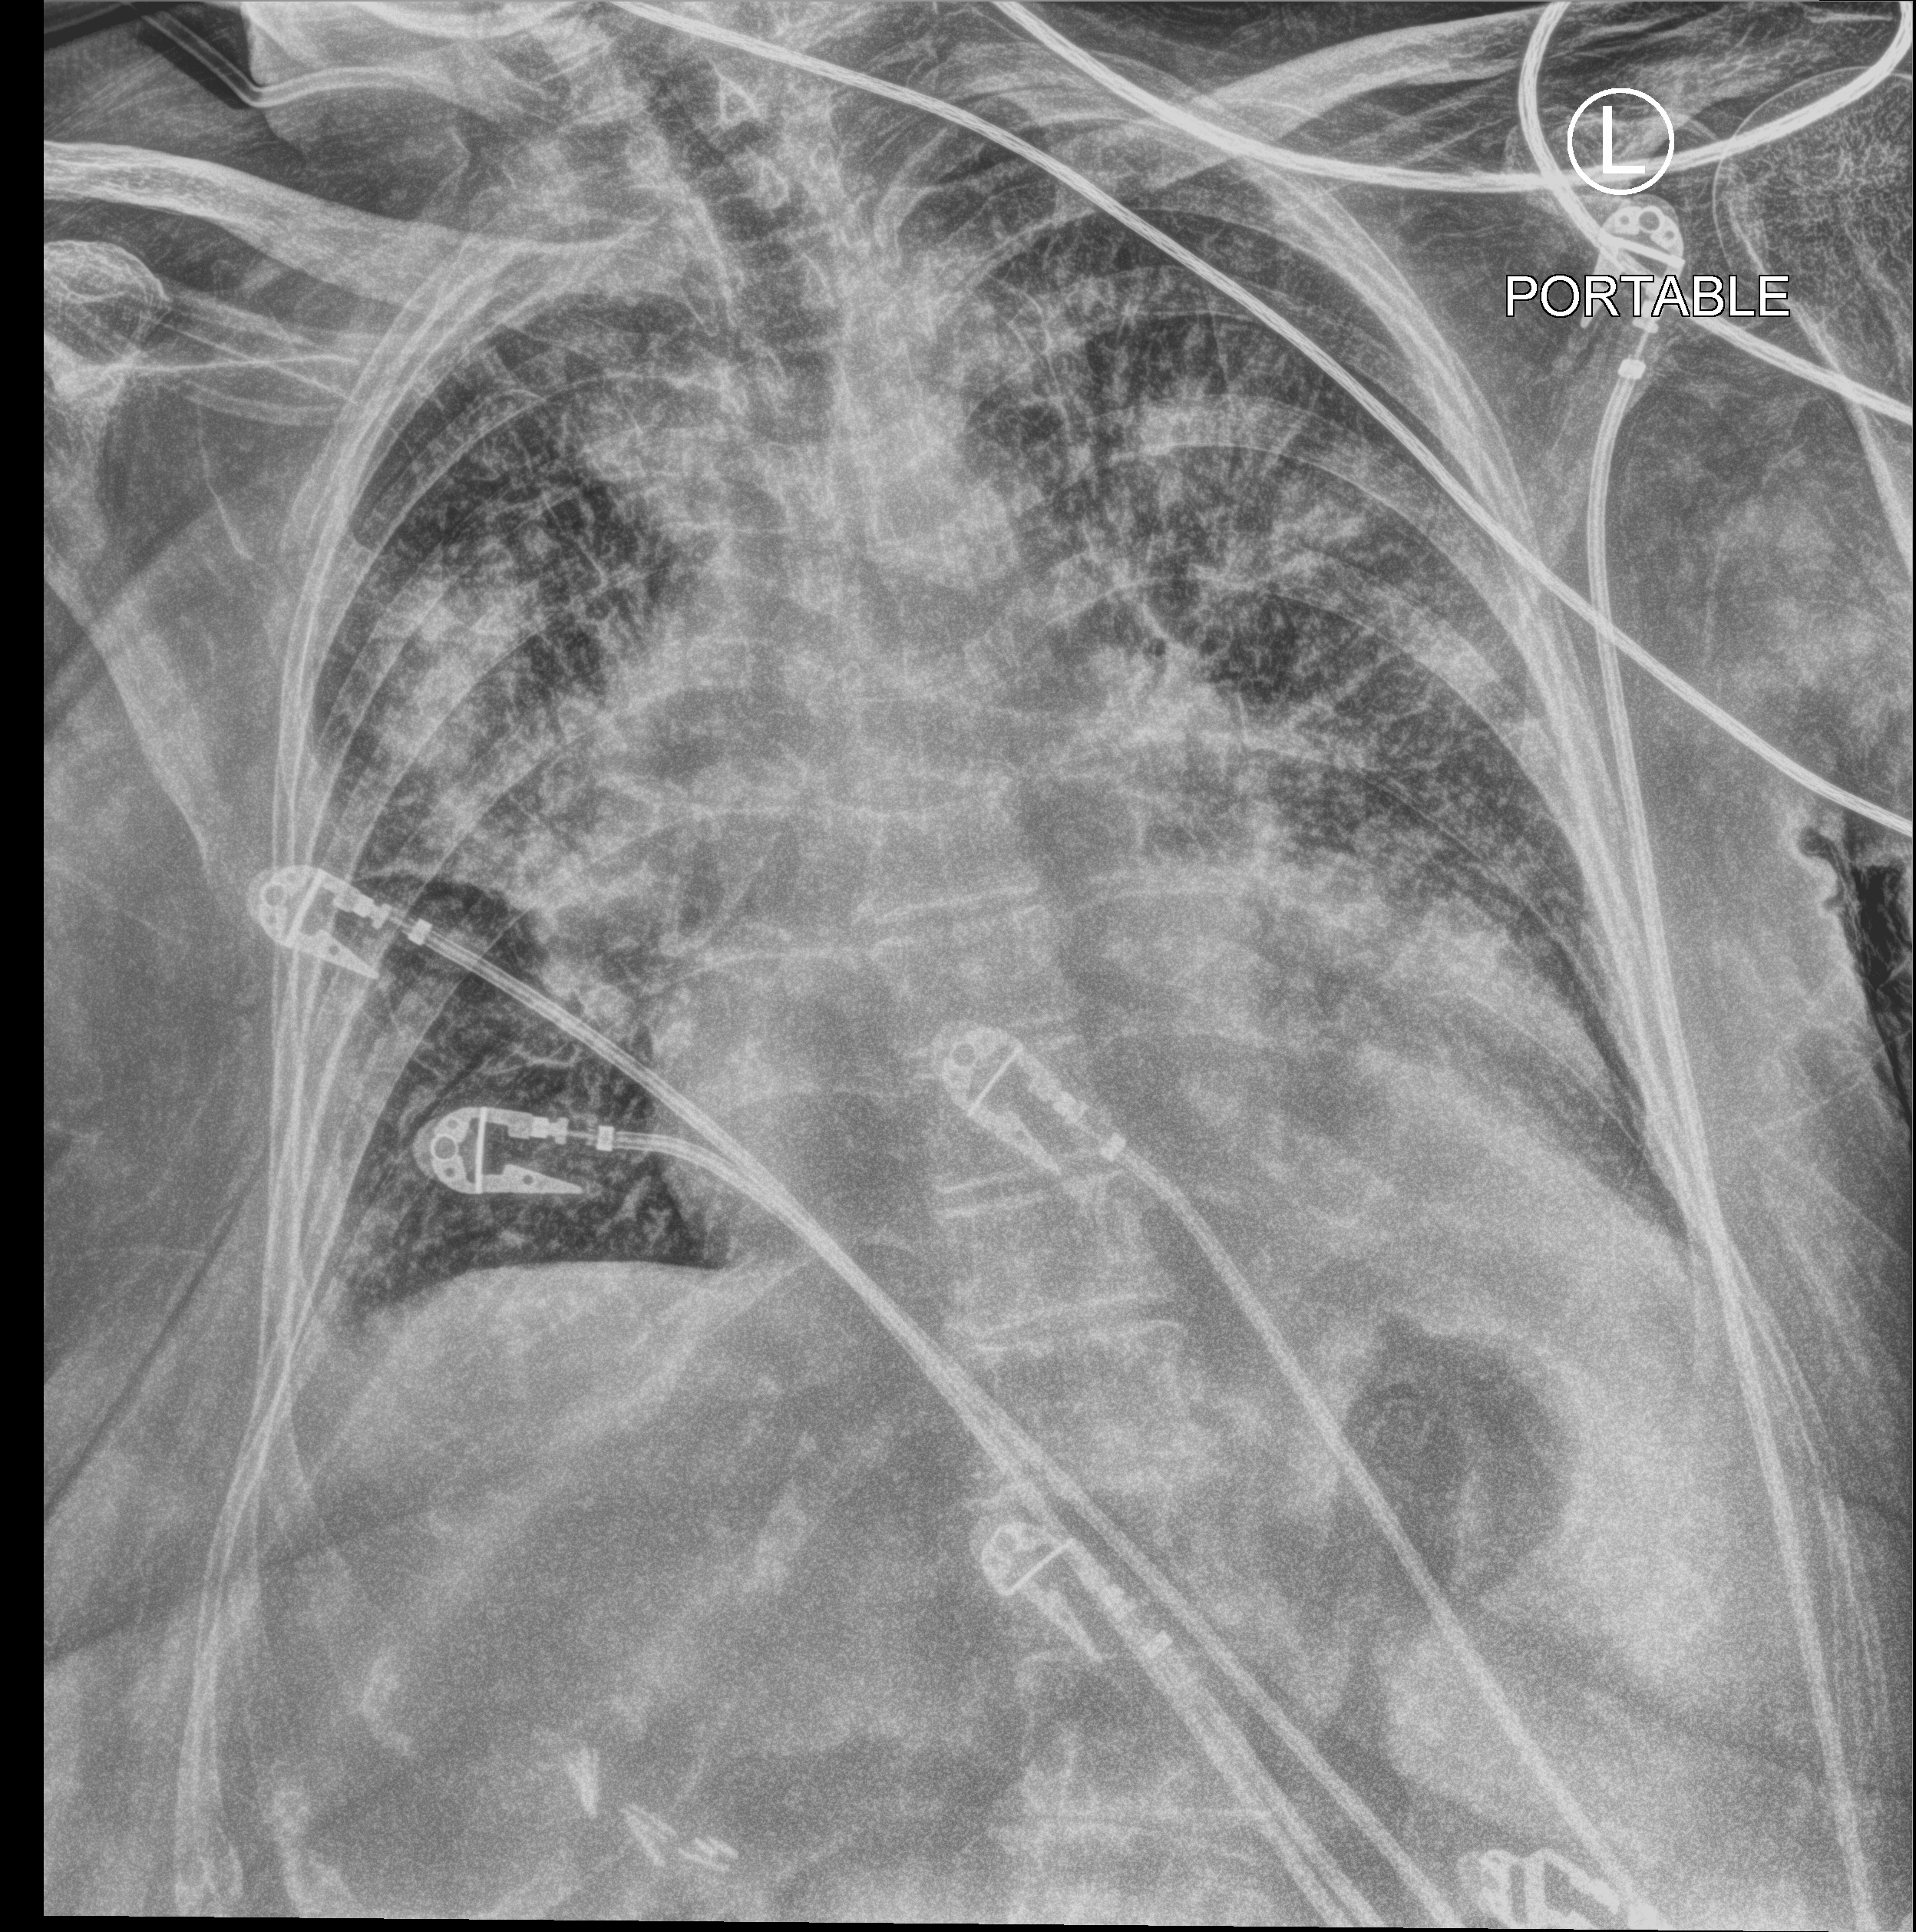
Chest X-ray (portable), anteroposterior (AP) projection. Patient hospitalised with COVID-19; female, aged 75–90 years.
Hospital-stay facts (about this admission, not read from this image; timing relative to this image not recorded): admitted to intensive care during this hospital stay: no; COPD (admission record): no.